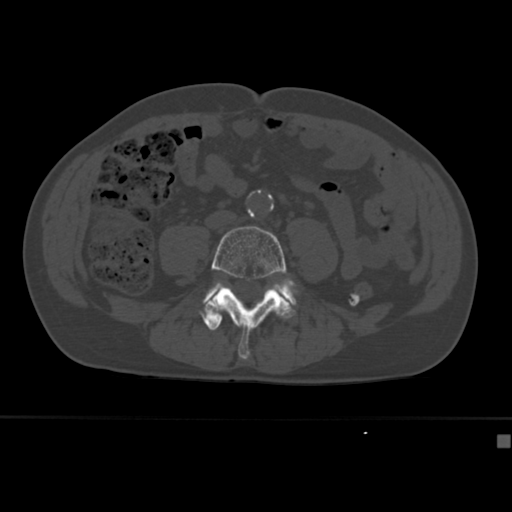
CT including the spine, one axial slice; position 103 of 430 along the scan axis; reconstruction kernel Br40s; bone window (W 1800 / L 400 HU); 512 × 512 image matrix, field of view 337 × 337 mm. Male patient, age 64 years. Case-level facts recorded for this patient, not image findings: primary cancer: uterus.
Structures marked on this image (semi-automatically segmented with operator editing):
- L4 vertebra: bounding box <204,226,296,360> (left, top, right, bottom; pixels)
- L5 vertebra: <203,278,298,306>